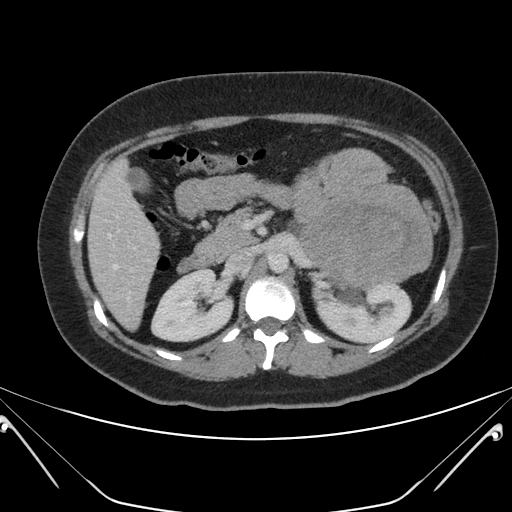
Contrast-enhanced abdominal CT, one axial slice; slice 118 of 168 in the series (ordered by position); intravenous contrast given; soft-tissue window (W 400 / L 40 HU); 512 × 512 image matrix. Female patient, age 26 years. From the clinical record (not read from this slice): diagnosis: adrenocortical carcinoma; tumour side: left adrenal; tumour size at pathology: 28 cm; Ki-67 index: 20 %; stage (as recorded): 2.
Annotated regions visible in this slice (semi-automatic segmentation, software-assisted and operator-edited):
- mass: bounding box [x1, y1, x2, y2] px = [292, 149, 433, 287]